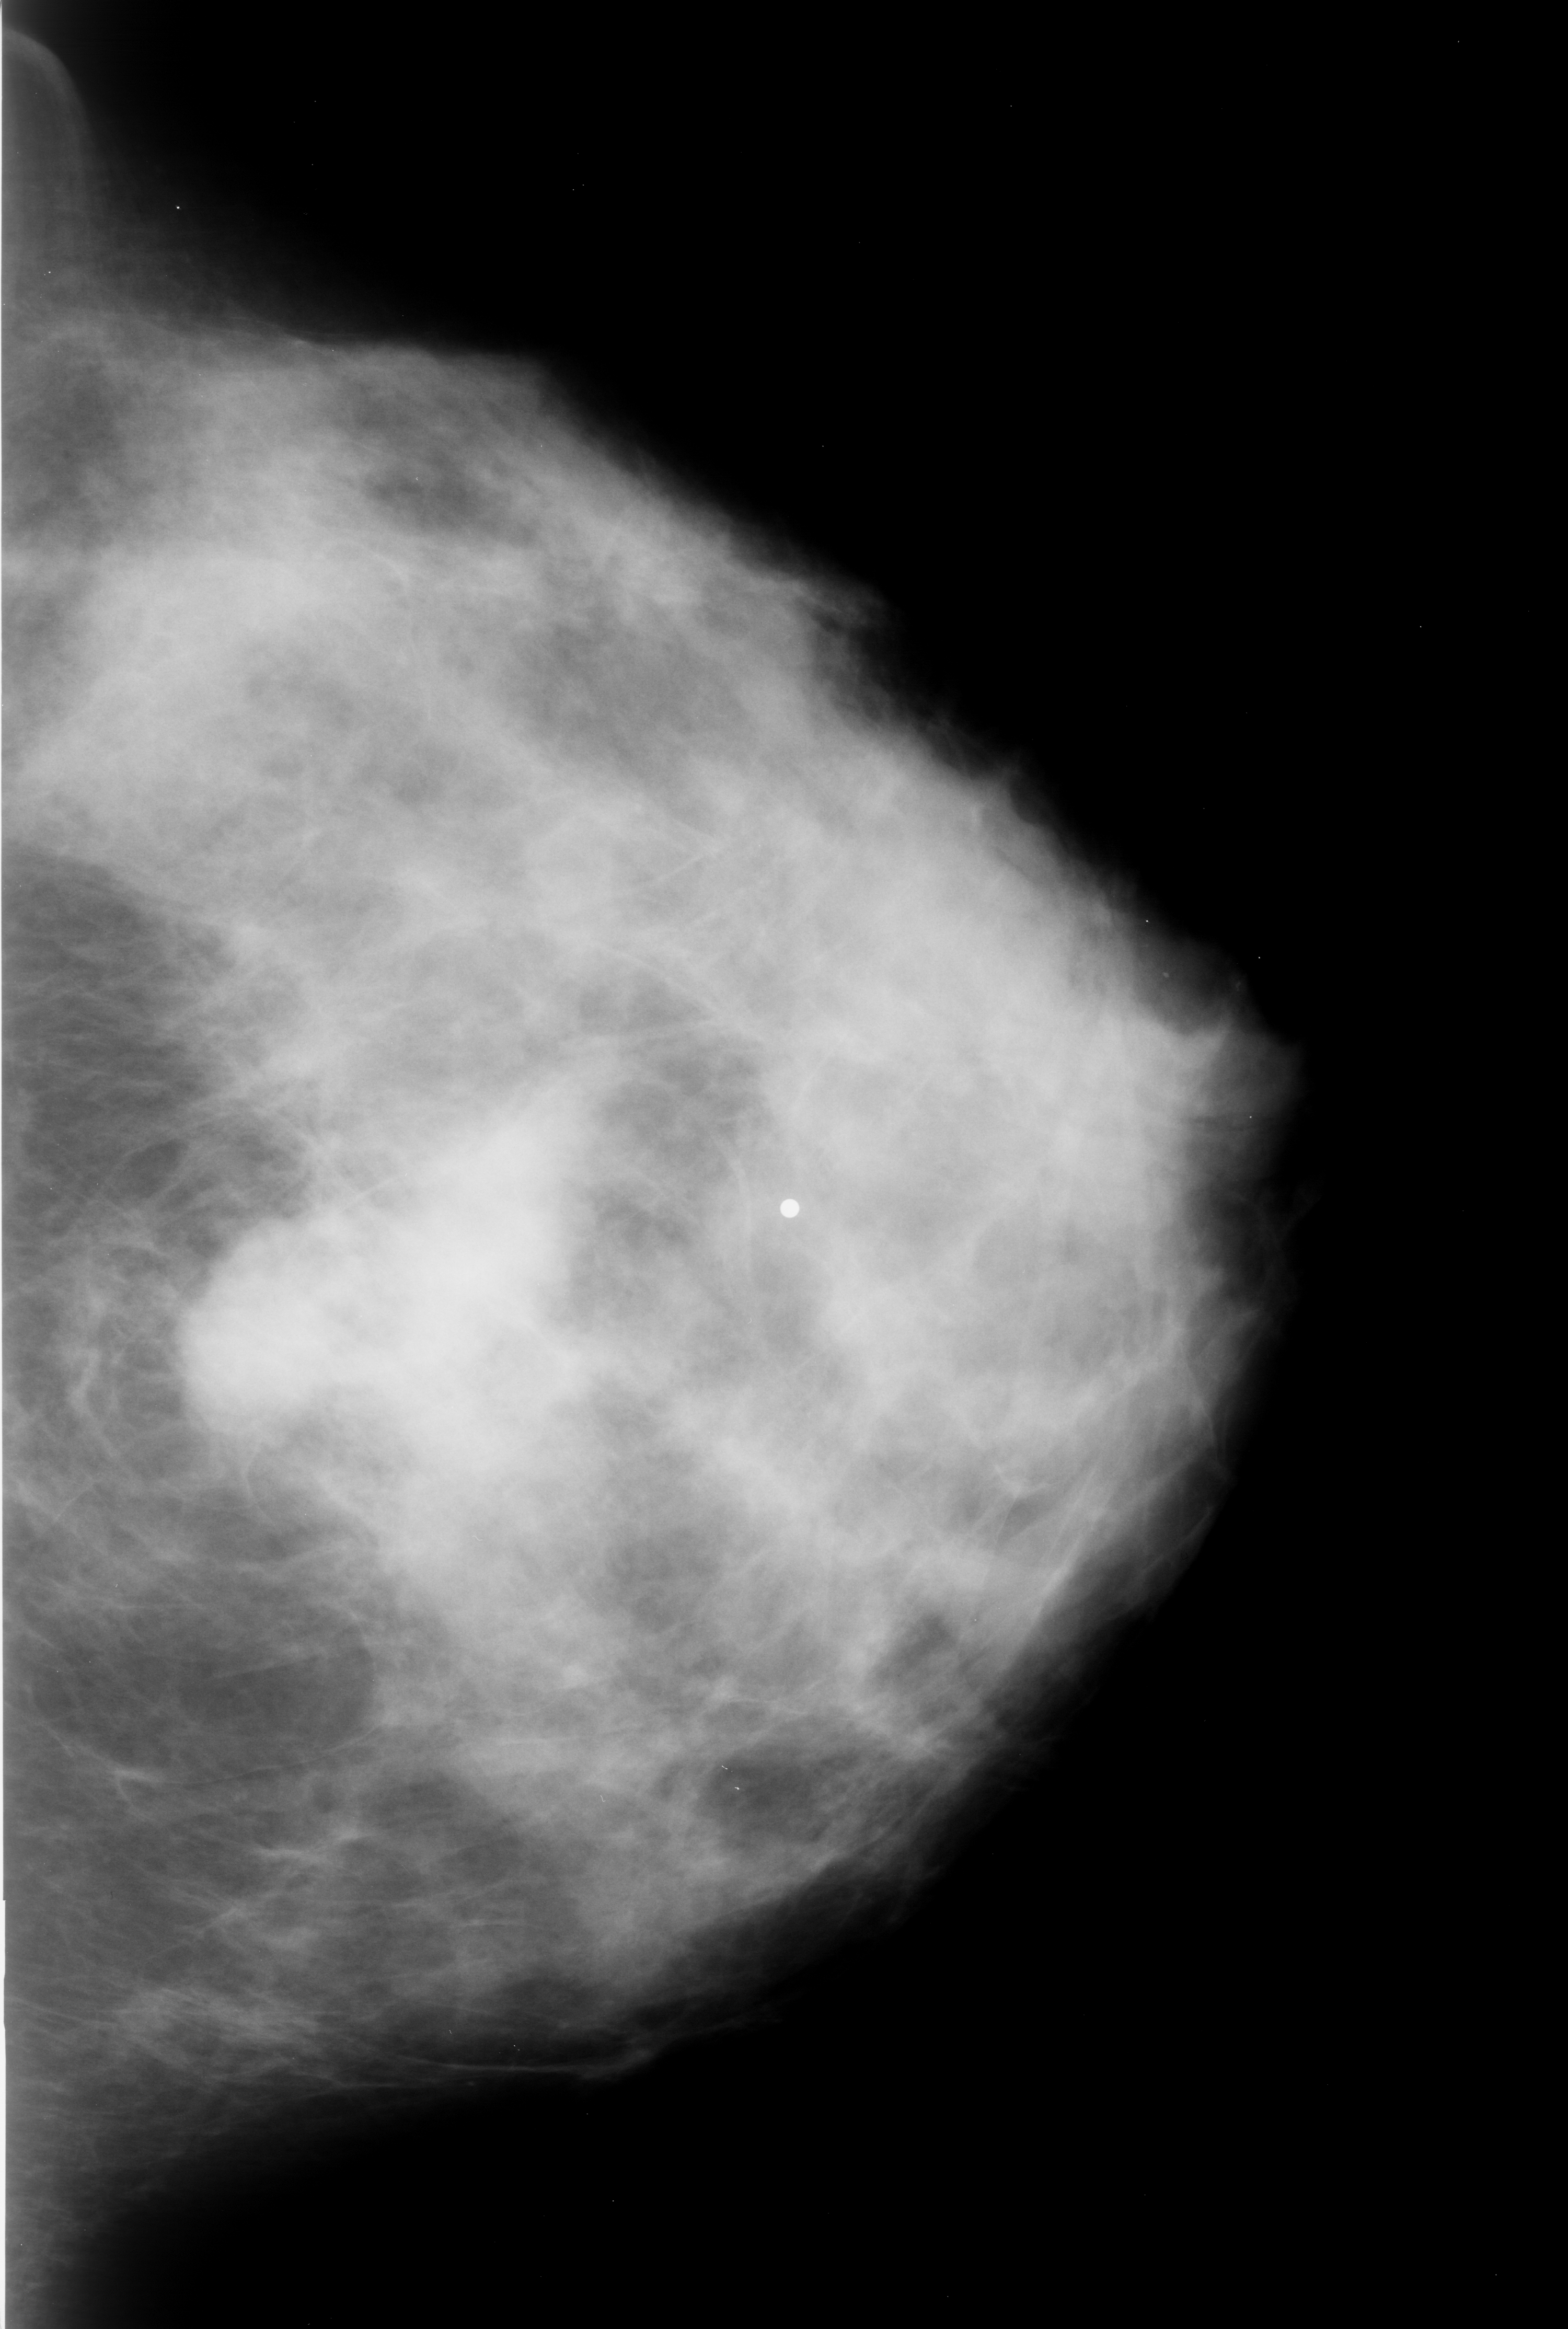
Scanned film-screen mammogram; left breast; craniocaudal (CC) view; breast composition: heterogeneously dense (BI-RADS density category 3 of 4); 1568 × 2329 image matrix.
Marked abnormalities (boxes around the expert regions of interest):
- mass, shape lobulated / irregular, margins obscured / ill defined; BI-RADS assessment category 4; subtlety rating 4 on a 1 (subtle) to 5 (obvious) scale; pathology (as recorded): malignant: bounding box <162,1232,373,1434> (left, top, right, bottom; pixels)